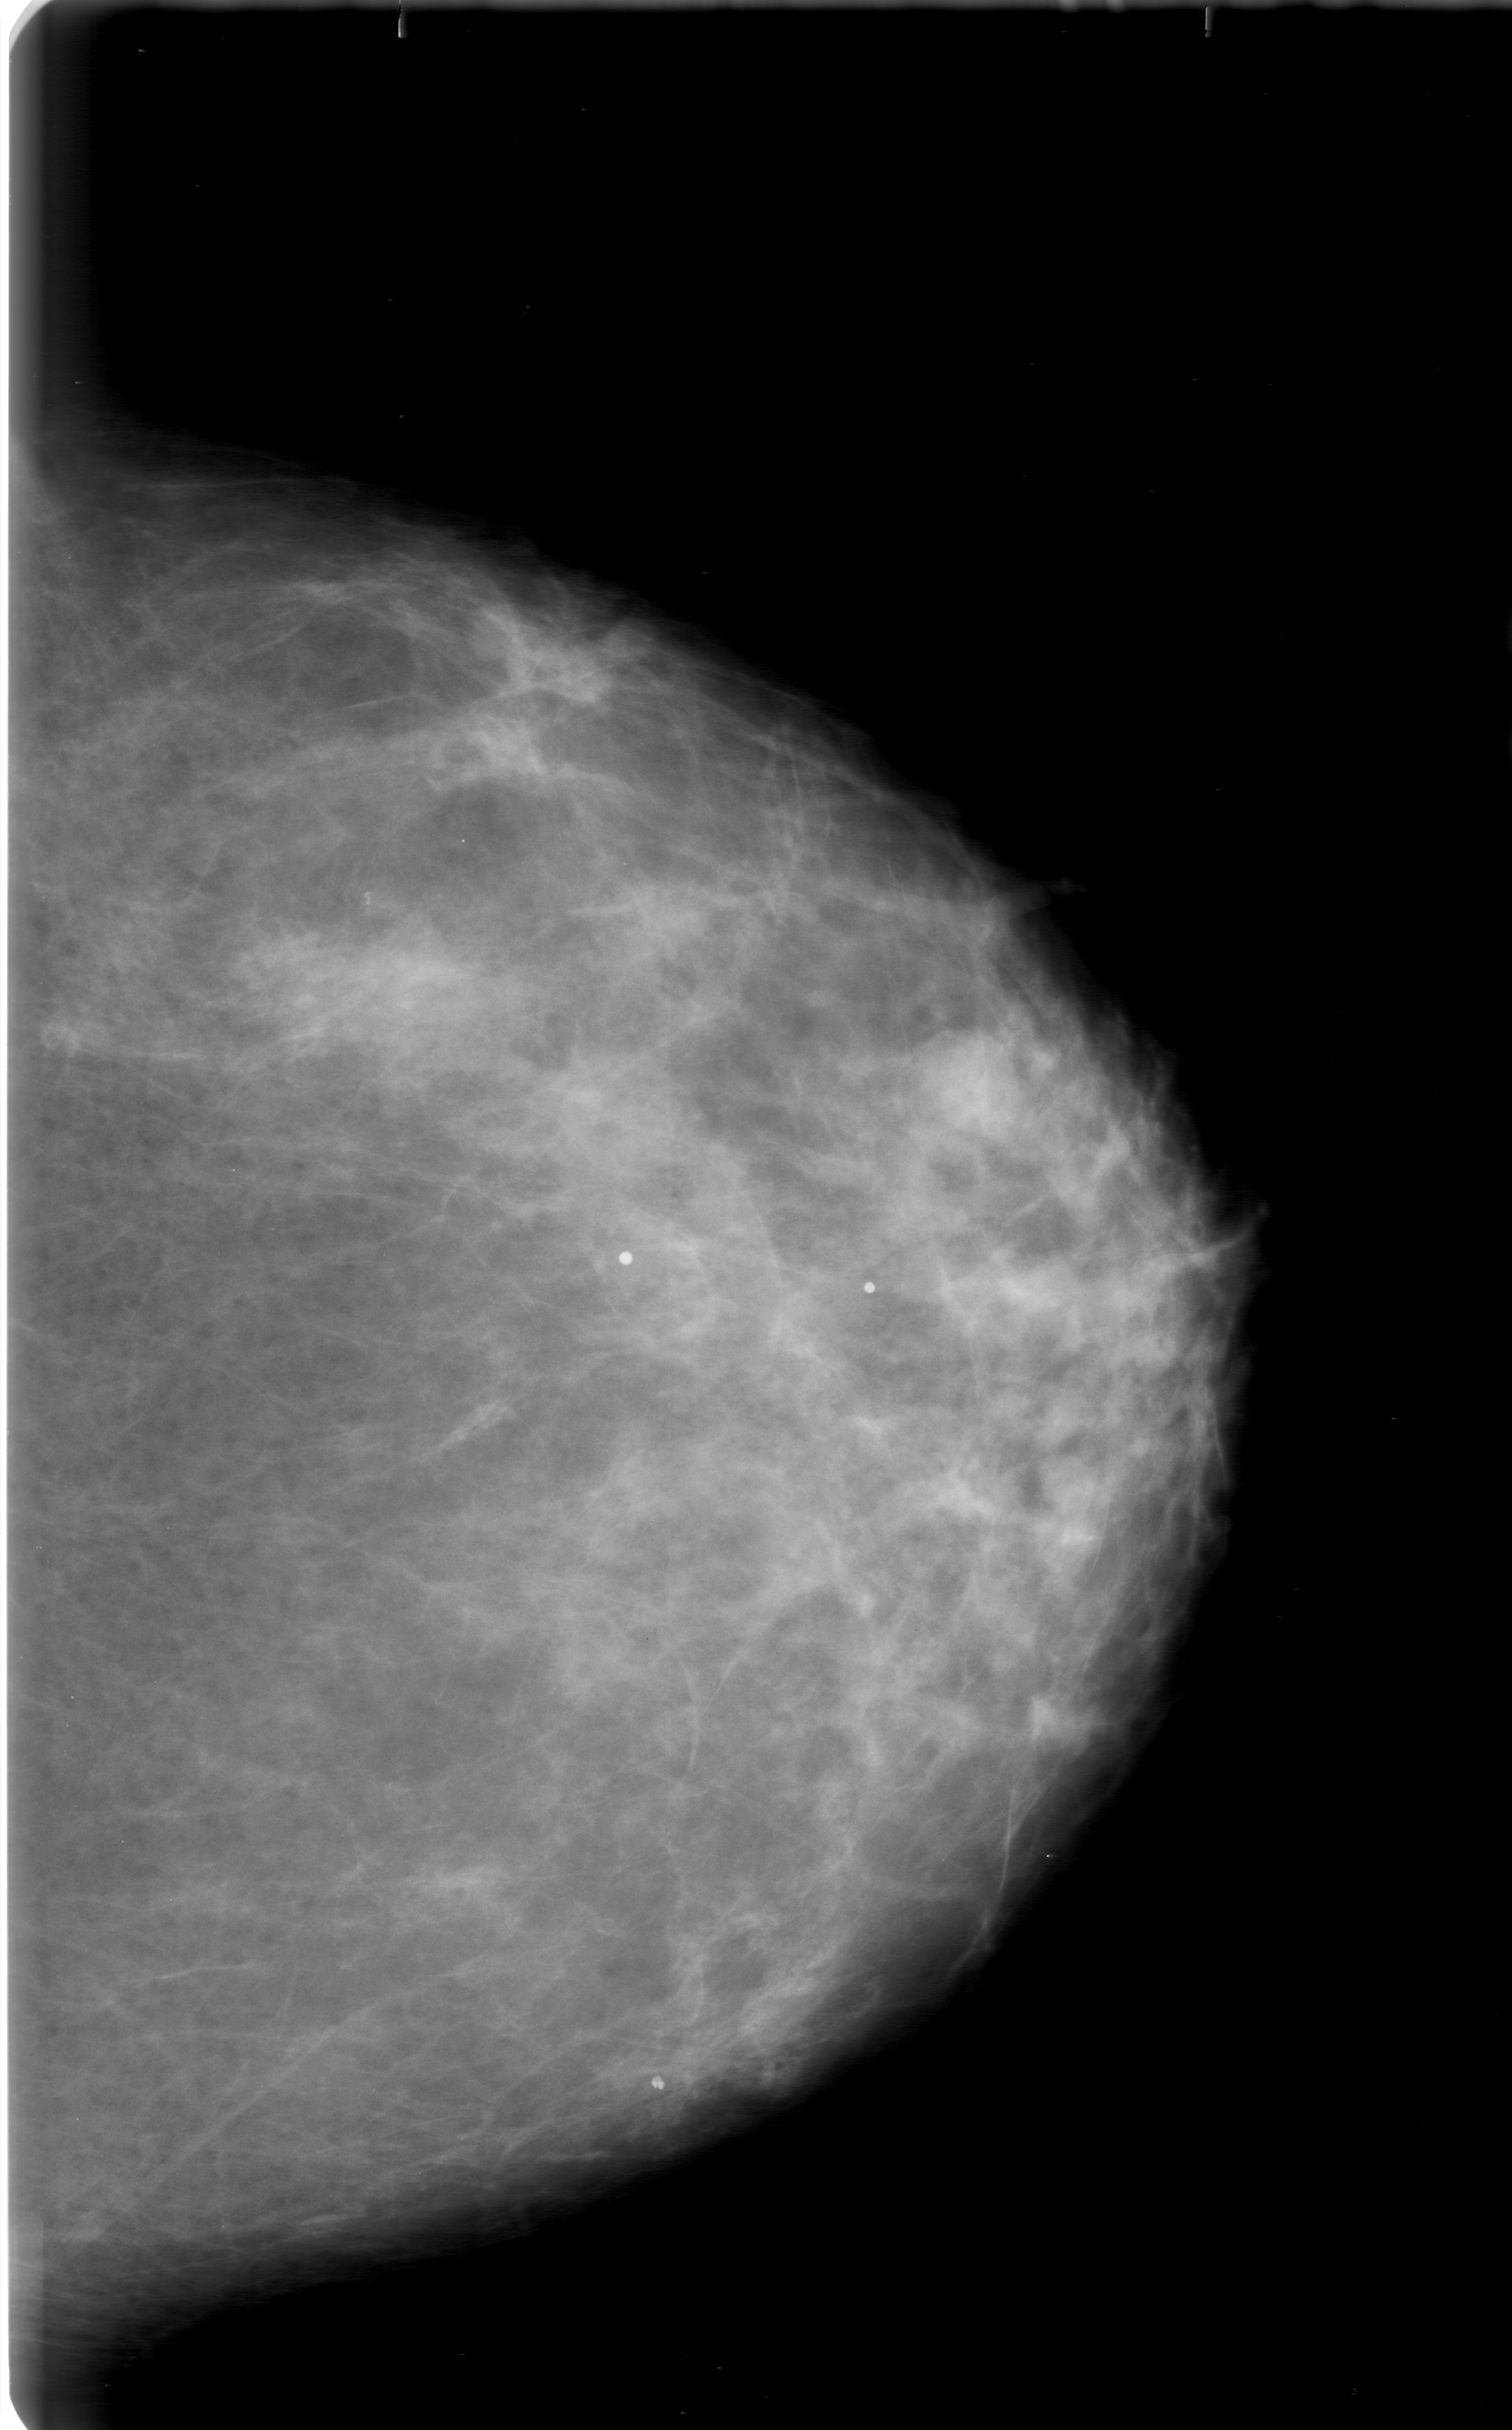
Mammogram (digitized film); left breast; craniocaudal (CC) view; BI-RADS breast density category 2 (scale 1–4); 1512 × 2430 image matrix.
Expert-marked regions of interest on this film, with their recorded descriptors:
- mass, shape oval, margins obscured; BI-RADS assessment category 0; pathology (as recorded): benign: box from (x=905, y=1019) to (x=1049, y=1184) px